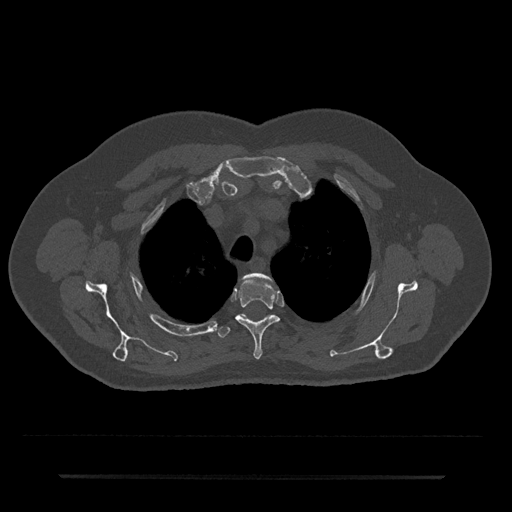
CT including the spine, one axial slice; slice 563 of 797 in the series (ordered by position); reconstruction kernel Br40s/3; bone window (W 1800 / L 400 HU); 0.5 mm slice thickness; 512 × 512 image matrix. Patient: male, 69 years. From the clinical record (not read from this slice): primary cancer: prostate.
Structures marked on this image (semi-automatically segmented with operator editing):
- T2 vertebra: box from (x=245, y=274) to (x=271, y=281) px
- T3 vertebra: (x=235, y=277)–(x=279, y=360)
- T4 vertebra: (x=218, y=315)–(x=245, y=338)